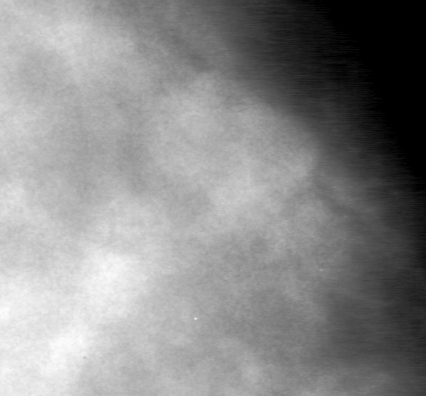
Cropped region of a digitized screen-film mammogram centred on a radiologist-marked abnormality, left breast, CC view, BI-RADS breast density category 3 (scale 1–4).
- Finding: mass, shape lobulated, margins microlobulated; BI-RADS assessment category 0 (incomplete: needs additional imaging); subtlety rating 3 on a 1 (subtle) to 5 (obvious) scale; pathology result (as recorded, not read from the image): benign.